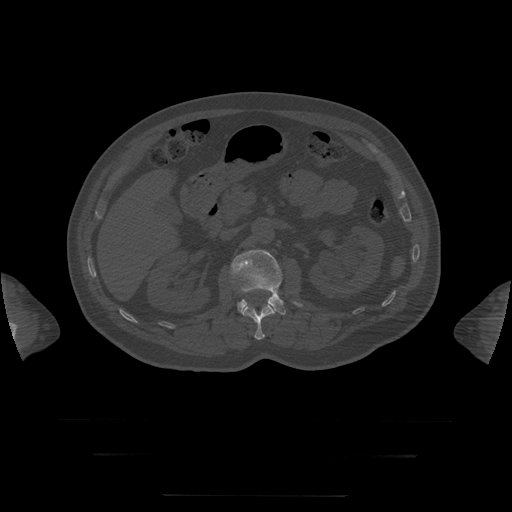
CT including the spine, one axial slice; position 35 of 397 along the scan axis; bone window (W 1800 / L 400 HU); 1.25 mm slice thickness; 512 × 512 image matrix, field of view 510 × 510 mm. Patient age 73 years. From the clinical record (not read from this slice): primary cancer: prostate.
Structures marked on this image (semi-automatic segmentation, software-assisted and operator-edited):
- L1 vertebra: bounding box (x1, y1, x2, y2) in pixels: (243, 303, 275, 340)